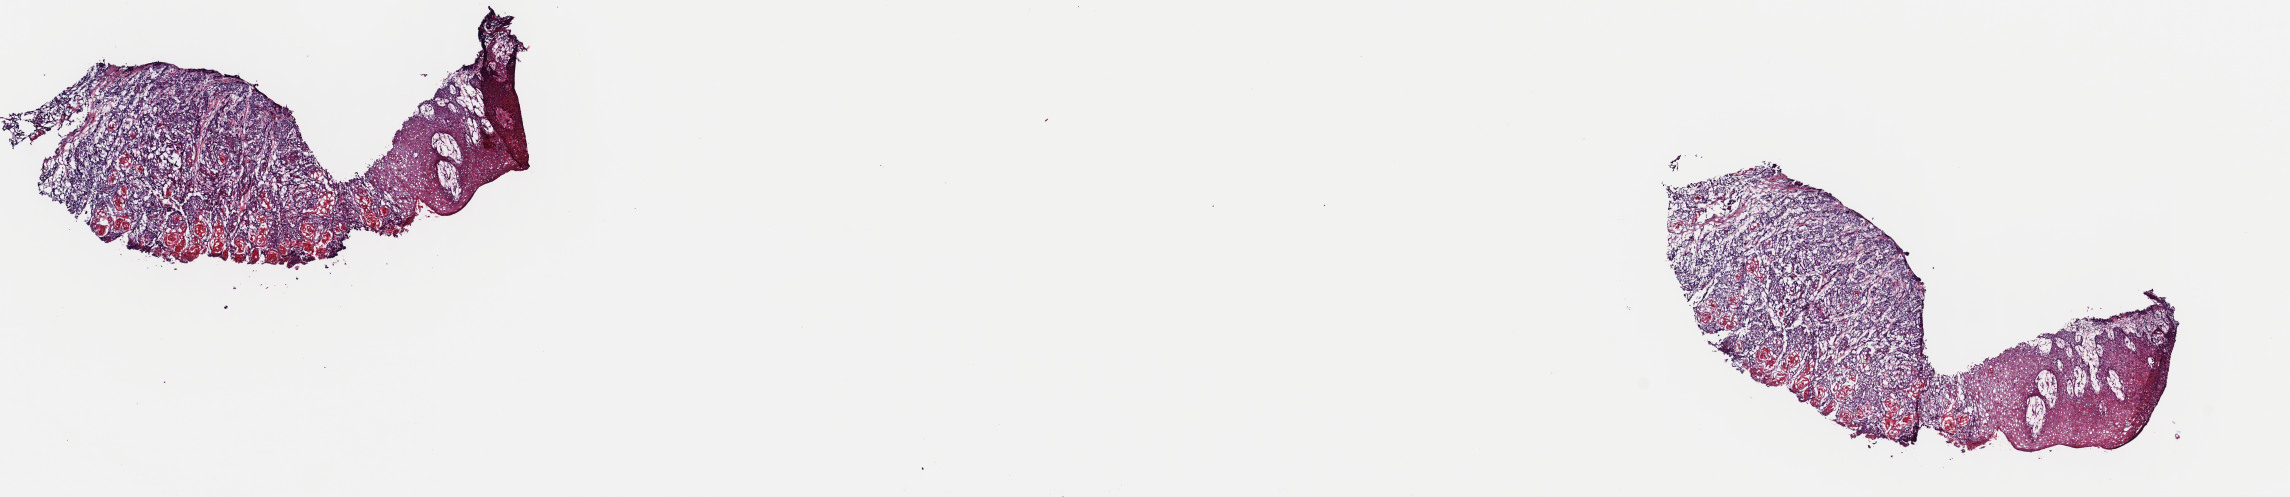
Whole-slide histology image, H&E-stained — a low-resolution overview of the entire scanned area, about 18.1 x 3.9 mm (acquisition: 40x scan). Frozen section from the top of the tissue portion. Sample: primary tumour, head and neck. Male patient; age at initial diagnosis 55 years. Histologic grade: G2 (moderately differentiated). Composition of this section per pathologist review: tumour cells 60%, tumour nuclei 65%, normal cells 40%, stromal cells 0%, necrosis 0%. Inflammatory infiltration, as recorded: lymphocyte infiltration 2%, monocyte infiltration 0%, neutrophil infiltration 0%.
Diagnosis: Squamous cell carcinoma, keratinizing, NOS (anterior floor of mouth). AJCC pathologic stage: II (7th edition).